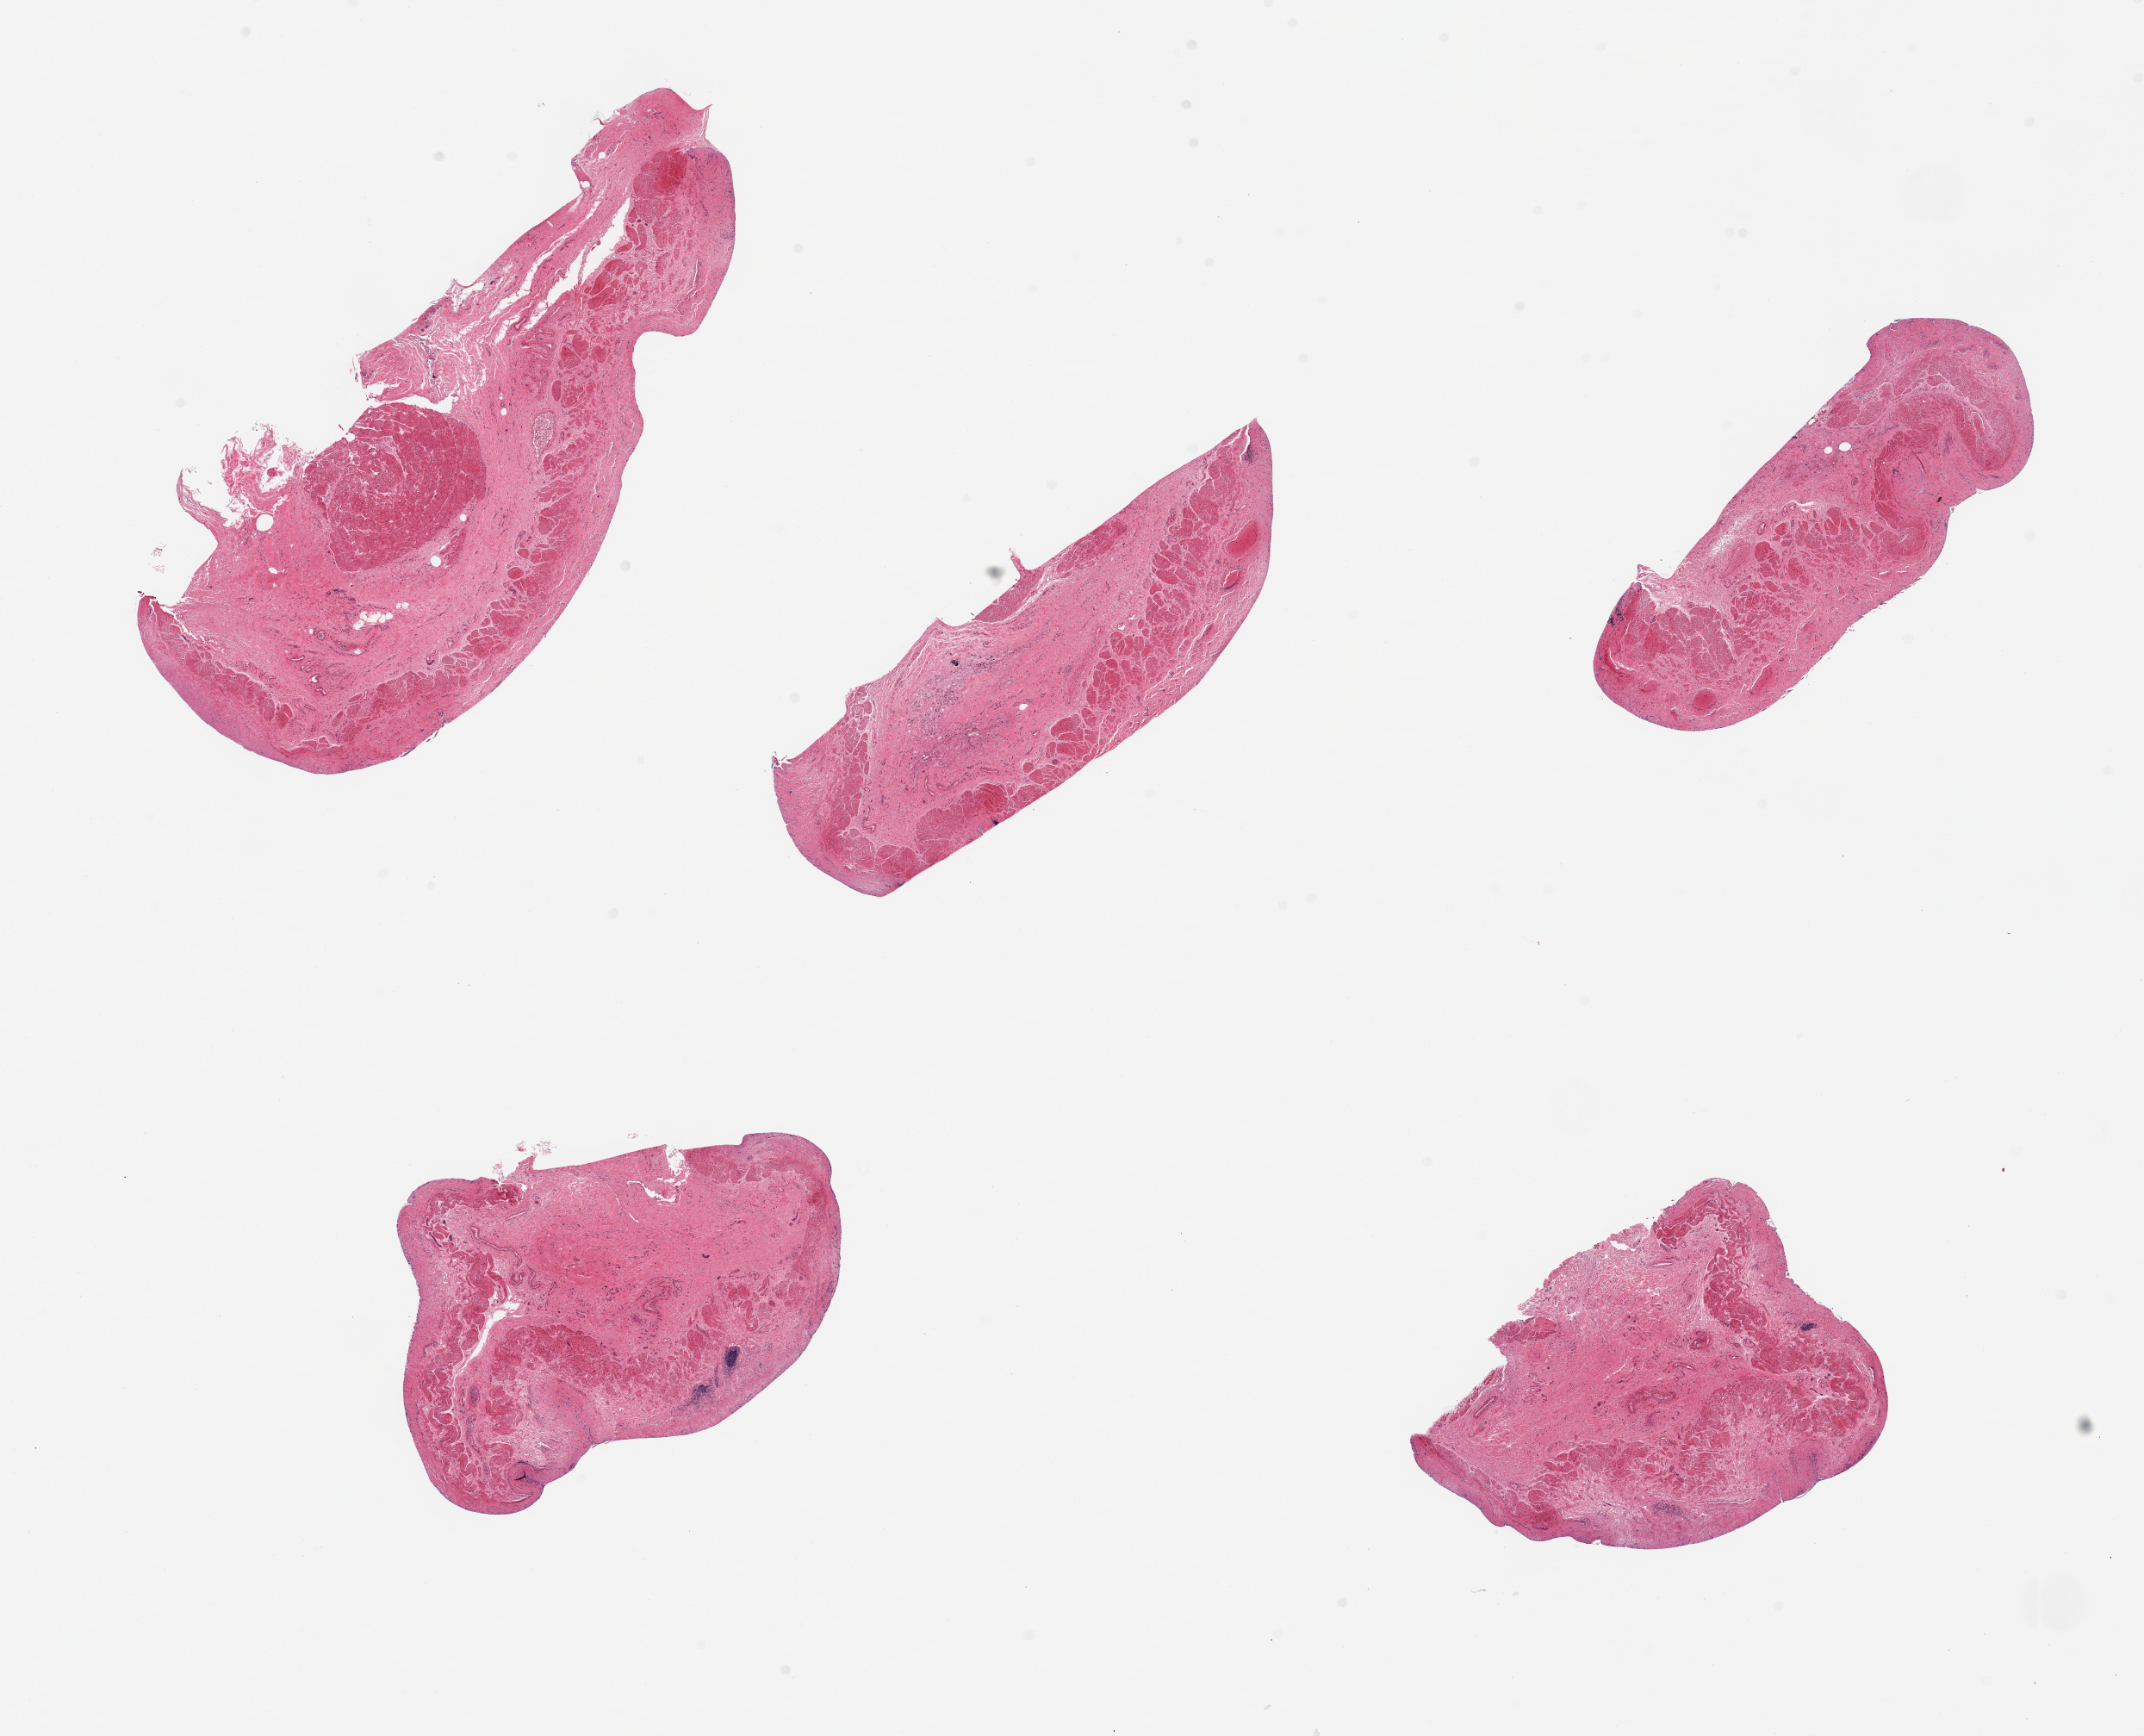
Hematoxylin and eosin (H&E) whole-slide image, brightfield, a low-resolution overview of the entire scanned area, about 19.7 x 15.9 mm (slide scanned at 20x). PAXgene-fixed paraffin-embedded (PFPE) section. Section of esophageal mucous membrane (target tissue). Donor tissue sample. Male donor.
Pathologist's review note for this sample: 6 pieces; autolyzed mucosa, predominantly smooth muscle/submucosa.